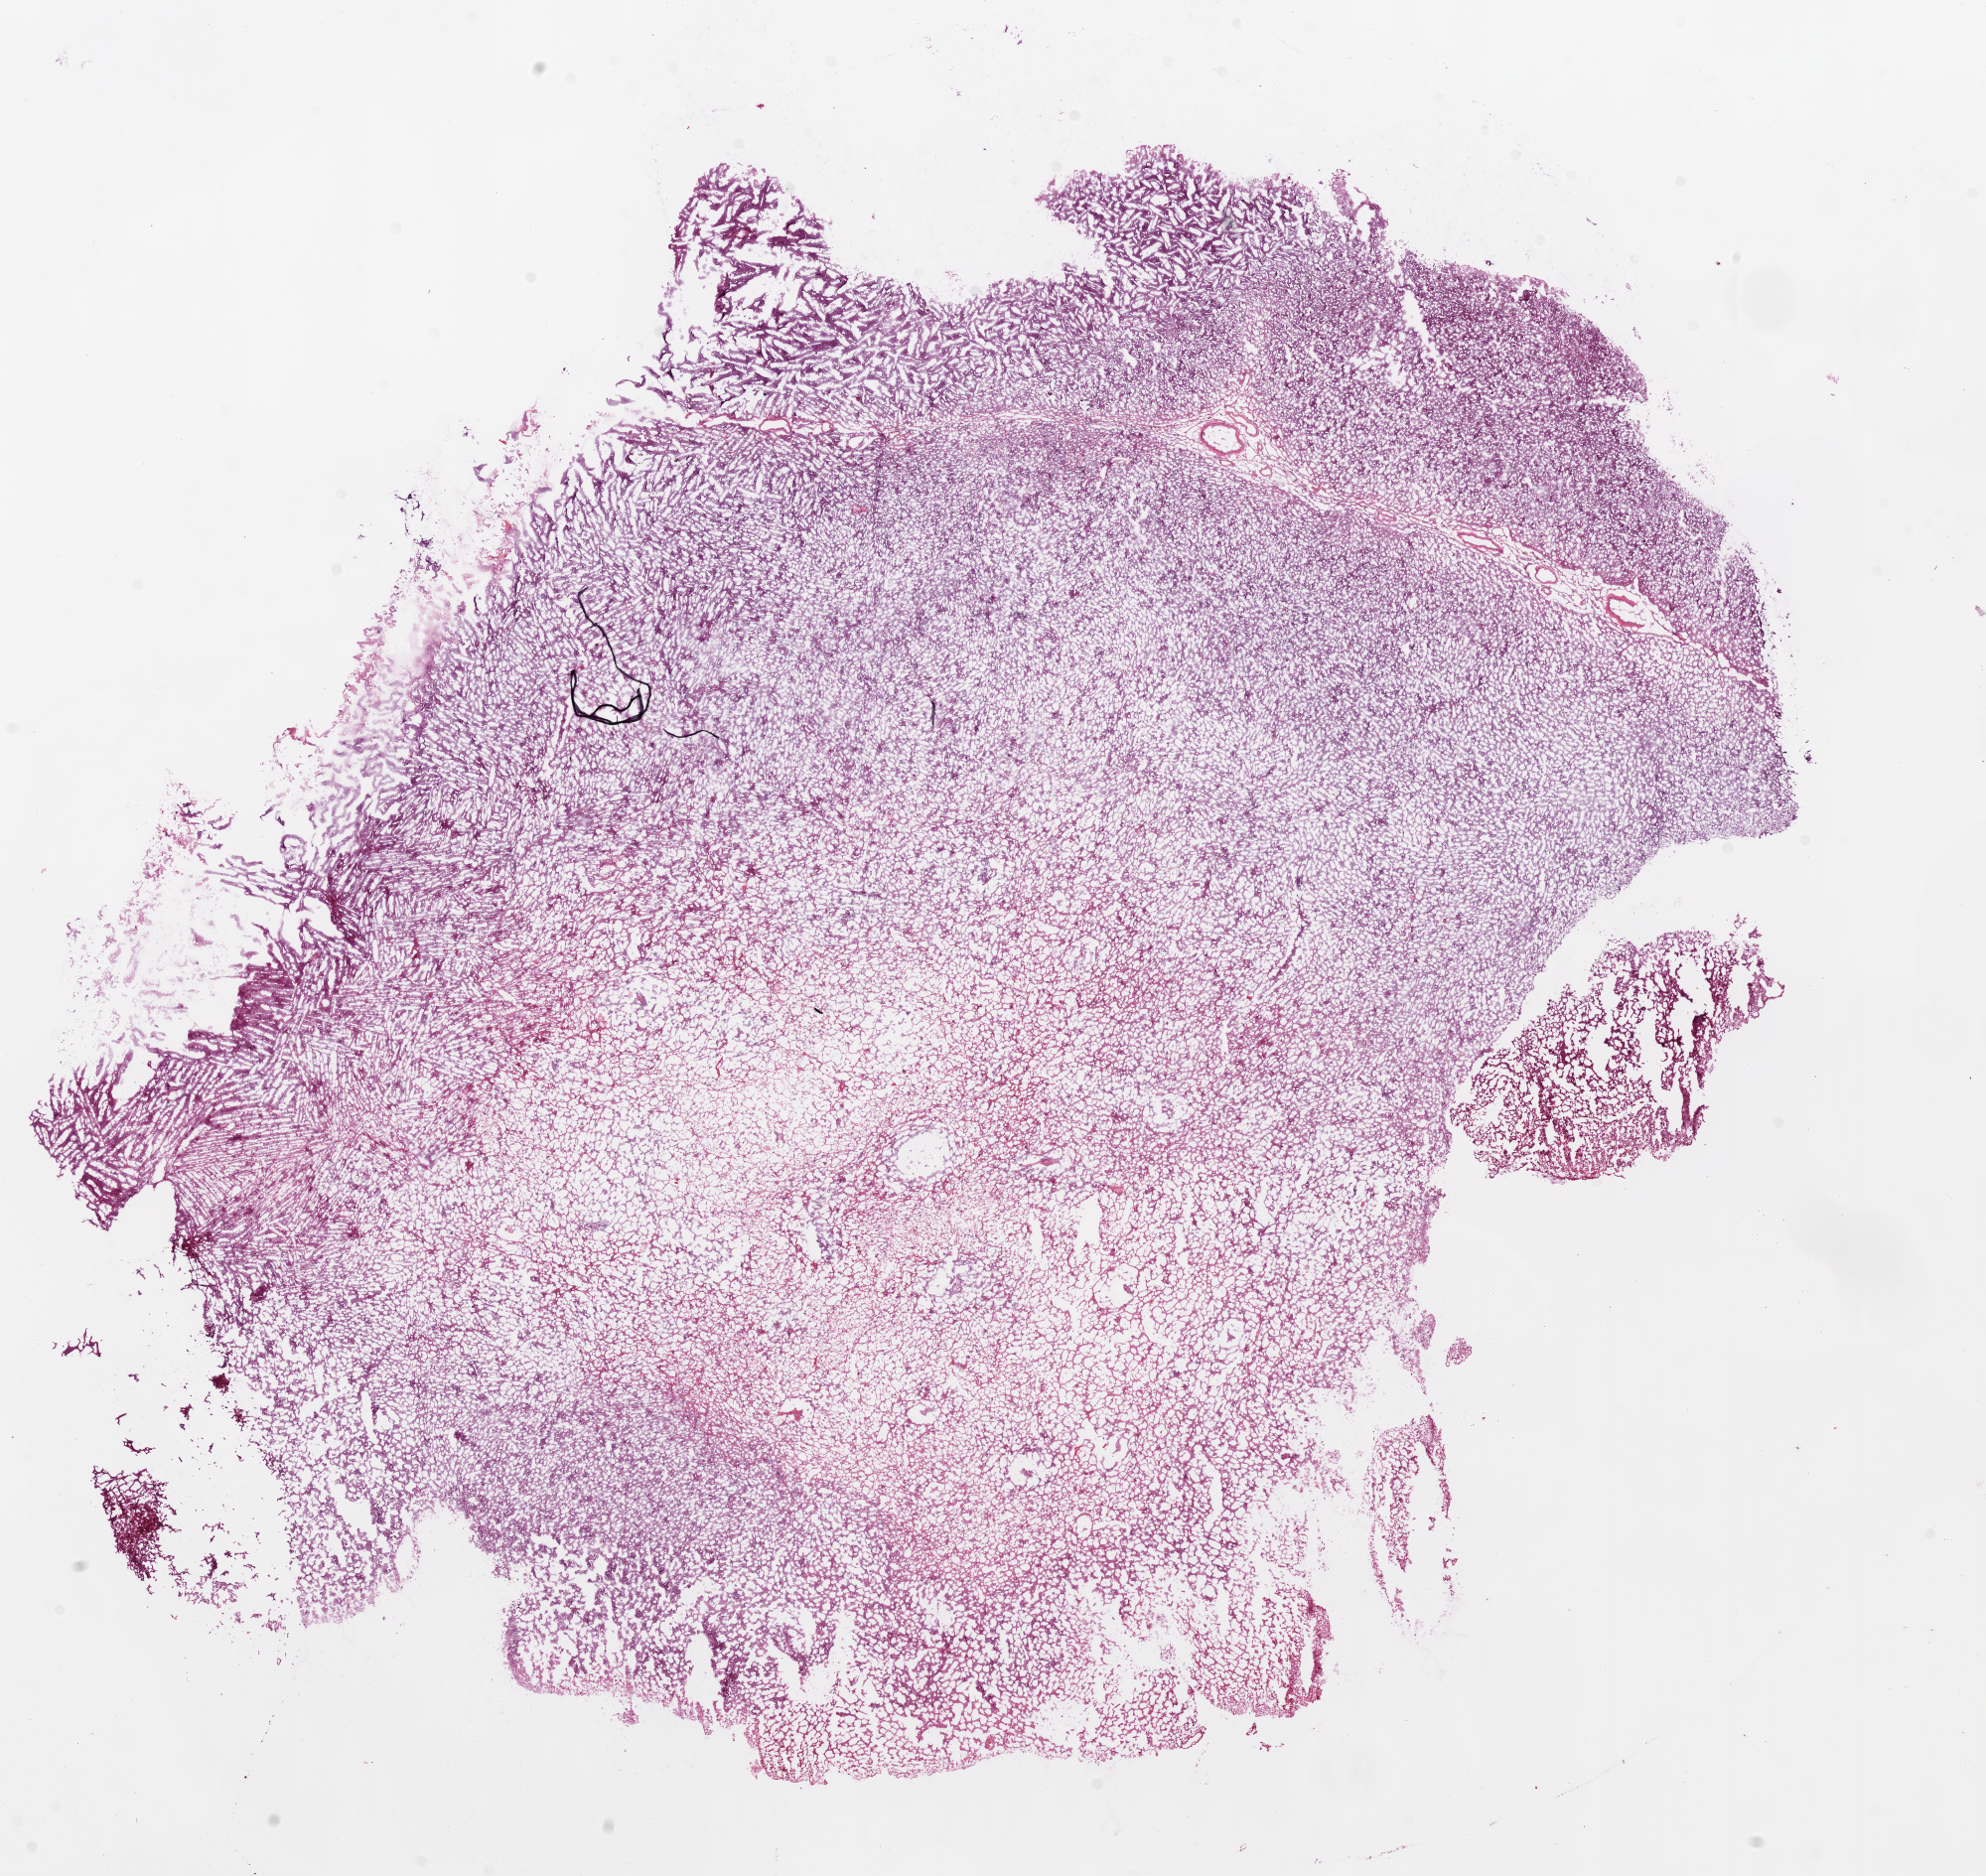
Whole-slide histology image, H&E — a low-resolution overview of the entire scanned area, about 16.0 x 15.2 mm. Frozen section from the top of the tissue portion. Primary tumour sample from the brain. Patient: male, age at initial diagnosis 57 years.
Pathologic diagnosis: Glioblastoma.